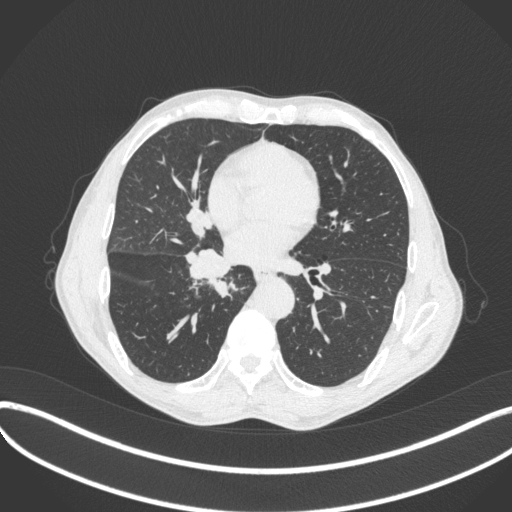
Chest CT, one axial slice; position 199 of 481 along the scan axis; 120 kVp; lung window (W 1500 / L -600 HU); 1 mm slice thickness; 512 × 512 image matrix, field of view 400 × 400 mm. Male patient, age 65 years. Case-level facts recorded for this patient, not image findings: clinical TNM (as recorded): T2a N0 M0; histopathological grade: G2.
Structures marked on this image (rectangle marked by the reading radiologist):
- lung tumour (recorded histology: squamous cell carcinoma): box from (x=181, y=245) to (x=237, y=282) px